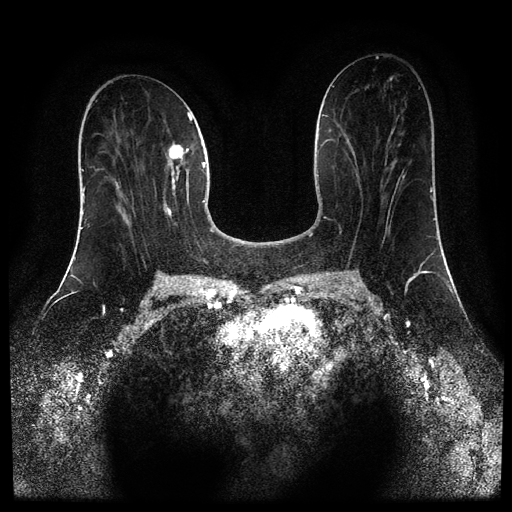
Breast MRI (dynamic contrast-enhanced, multi-phase), one axial slice; slice 42 of 110 in the series (ordered by position); dynamic contrast-enhanced series, time point 2 of 5 at this slice position (early post-contrast); 1.5 T; TE 2.6 ms, TR 5.4 ms; 512 × 512 image matrix. Patient: female, 43 years.
Outlined on this slice (semi-automatic segmentation, software-assisted and operator-edited):
- breast lesion (labelled 'tumour' in the annotation; benign lesions carry a separate 'benign' label): bounding box <163,144,184,219> (left, top, right, bottom; pixels)